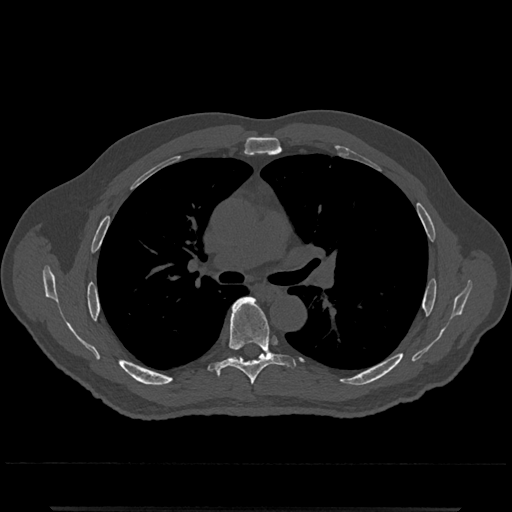
CT including the spine, one axial slice; position 773 of 797 along the scan axis; bone window (W 1800 / L 400 HU); 0.5 mm slice thickness; 512 × 512 image matrix, field of view 393 × 393 mm. Patient: male, 67 years. From the clinical record (not read from this slice): primary cancer: prostate.
Structures marked on this image (semi-automatic segmentation, software-assisted and operator-edited):
- T6 vertebra: box from (x=209, y=297) to (x=295, y=385) px